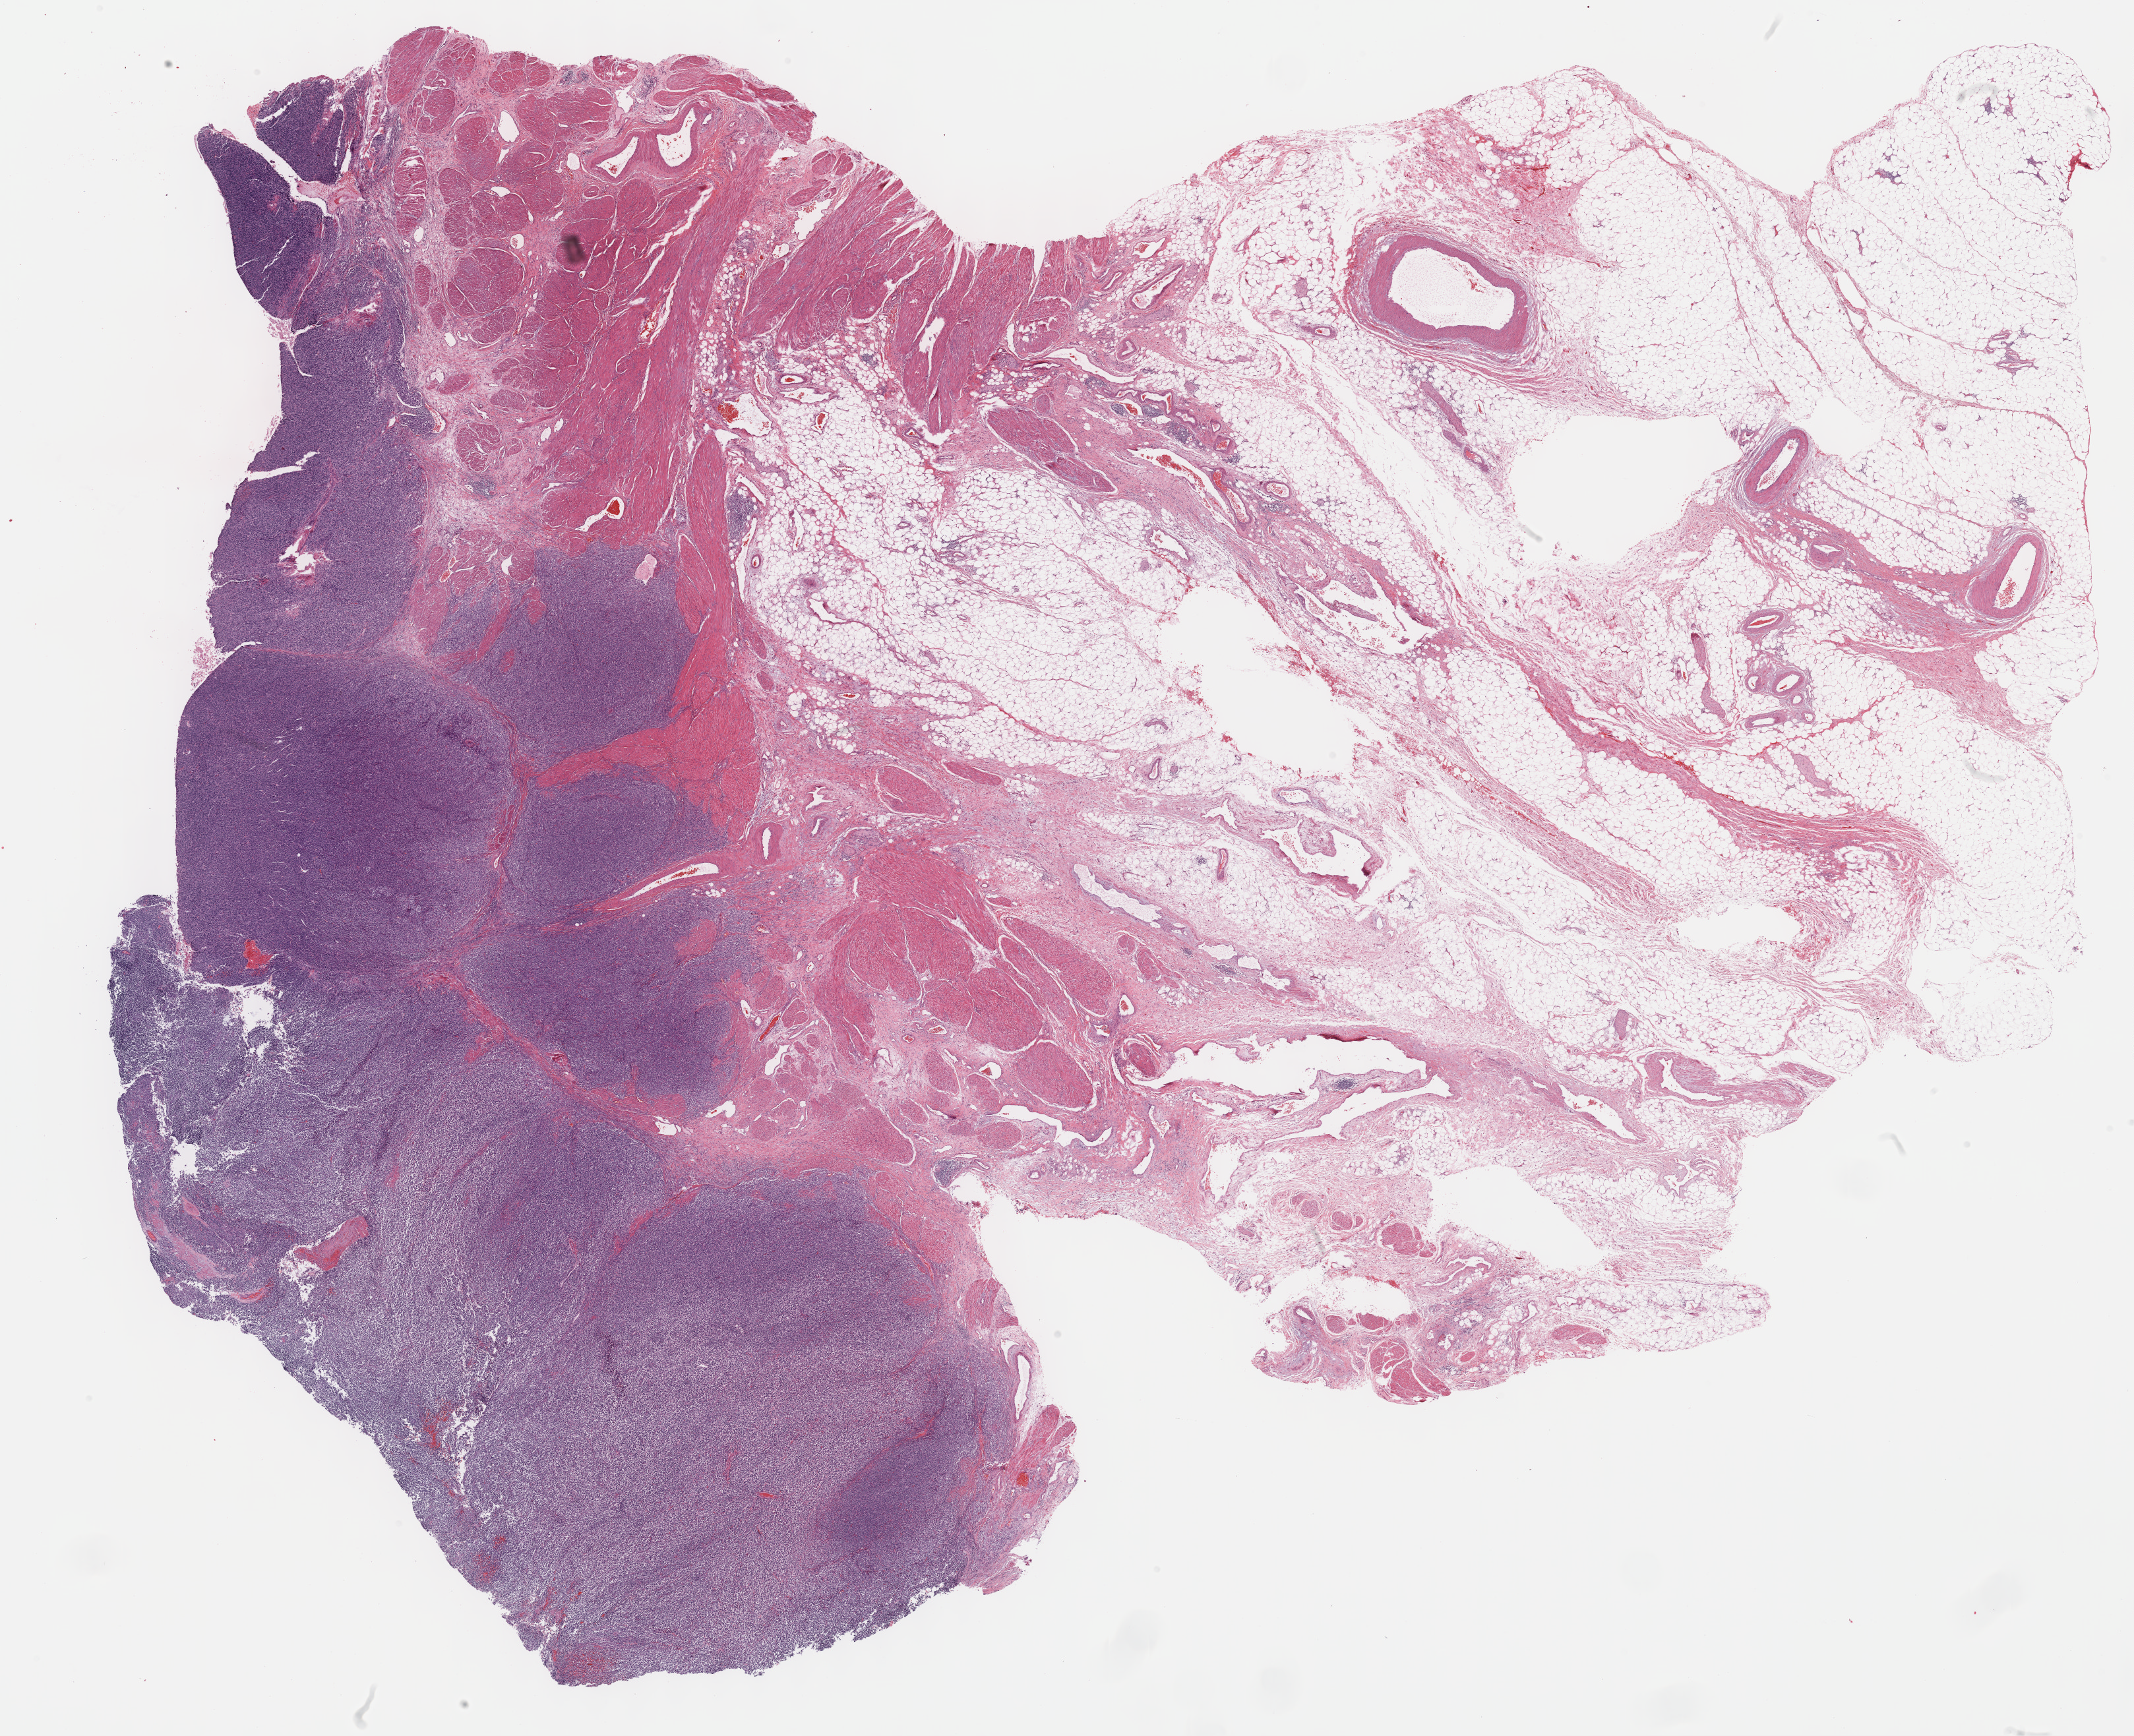
Digitized Hematoxylin and eosin (H&E) stained tissue section (whole slide) — a low-resolution overview of the entire scanned area, about 26.2 x 21.3 mm (acquisition: 40x scan); formalin-fixed paraffin-embedded (FFPE) diagnostic section; primary tumour sample from the bladder. Male patient; age at initial diagnosis 60 years. Histologic grade: high grade.
Lymph nodes positive (case pathology): 1 of 170 examined. AJCC pathologic stage: IV (5th edition). Histologic diagnosis: Transitional cell carcinoma.